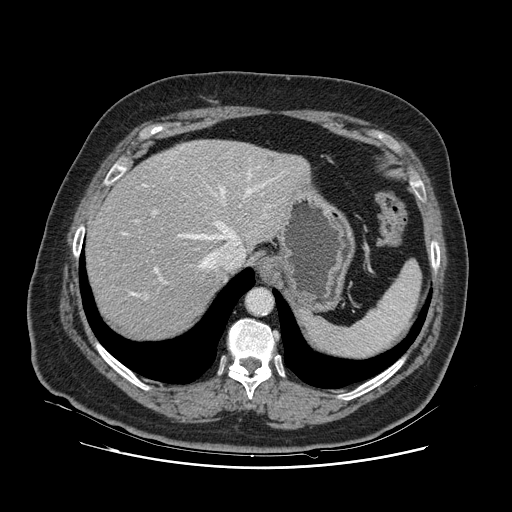
Contrast-enhanced abdominal CT, one axial slice; intravenous contrast given; soft-tissue window (W 400 / L 40 HU); 512 × 512 image matrix, field of view 391 × 391 mm. Female patient, age 73 years. Case-level facts recorded for this patient, not image findings: diagnosis: colorectal cancer liver metastases, imaged before liver resection; multiple liver metastases: no; largest metastasis: 7 cm; chemotherapy before resection: yes.
Annotated regions visible in this slice (manually delineated by an expert):
- hepatic veins: bounding box [x1, y1, x2, y2] px = [114, 171, 261, 299]
- liver: [87, 141, 306, 338]
- planned liver remnant (the part of the liver to remain after resection): [87, 161, 228, 339]
- portal vein (with intrahepatic branches): [153, 210, 158, 274]